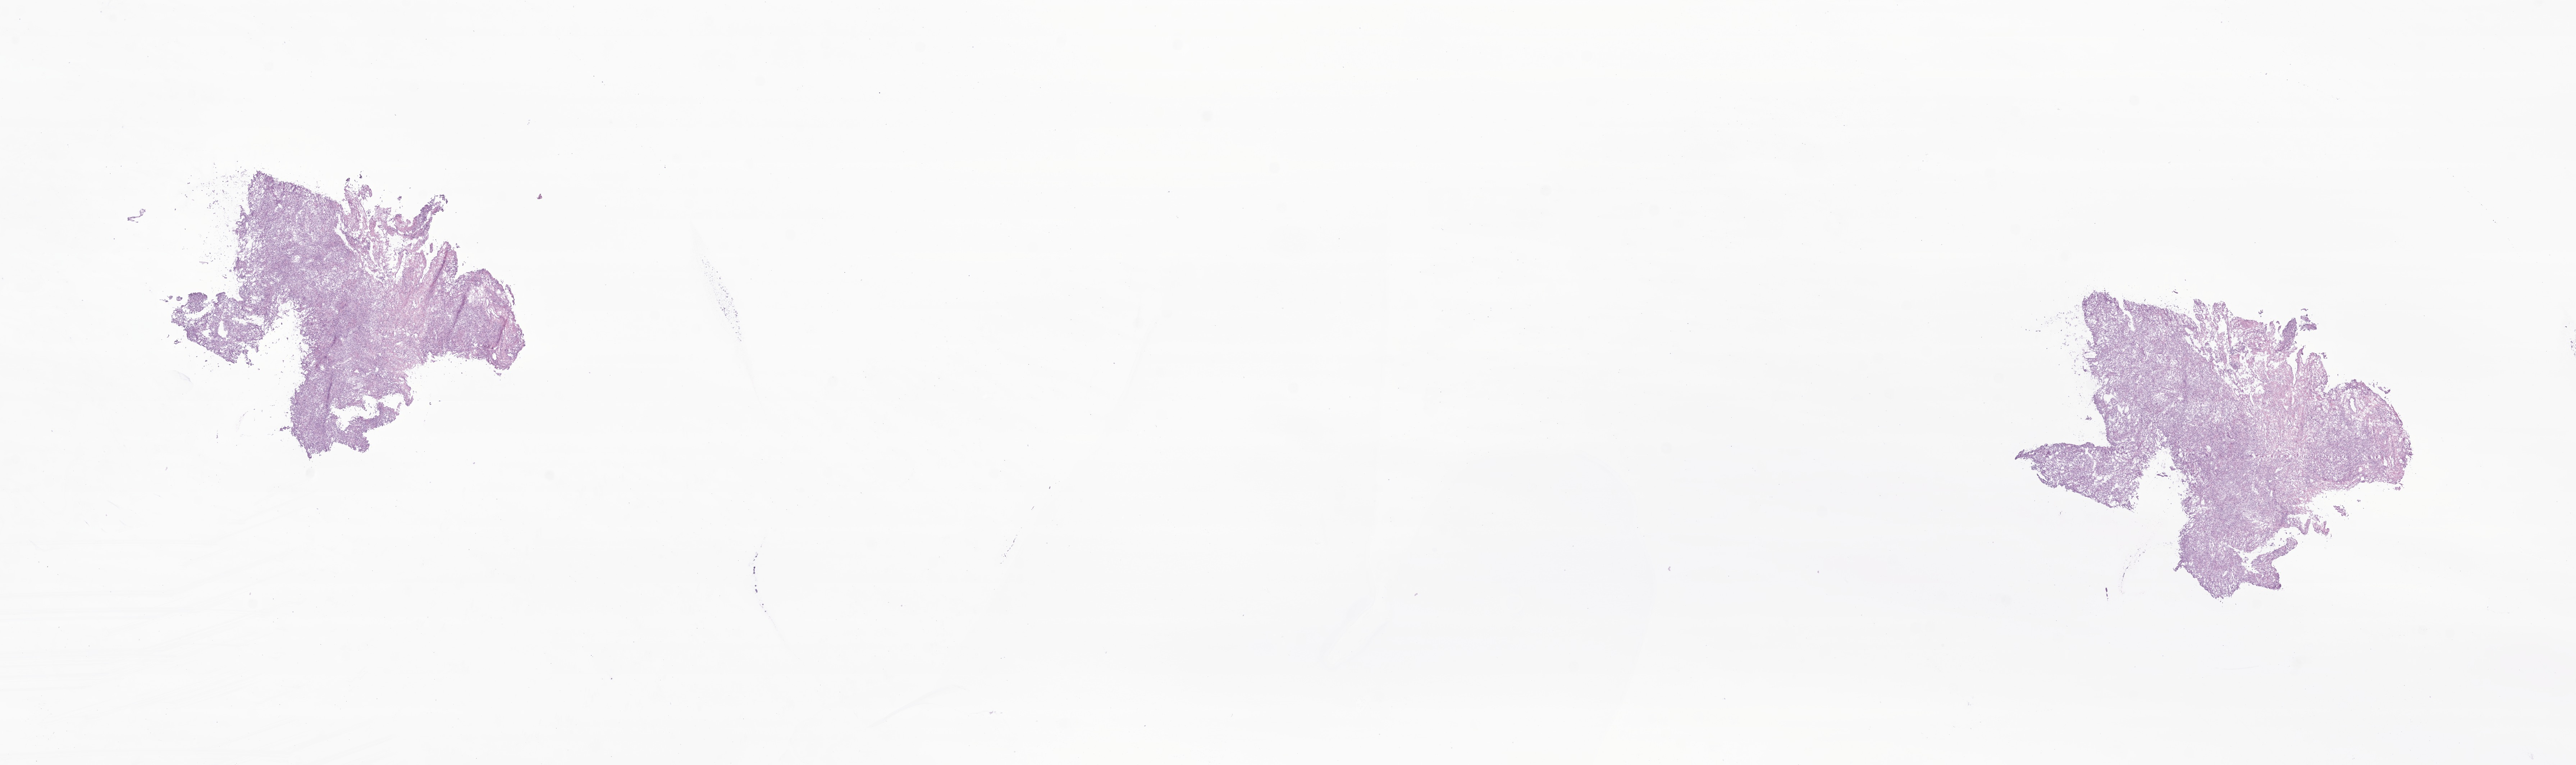
Whole-slide image, haematoxylin and eosin stain of tumor tissue from the ovary — whole scanned area (about 30.2 x 9.0 mm) shown as a low-resolution overview; frozen section. Patient female; age 187 months (15 years 7 months).
- recorded diagnosis: Sclerosing stromal tumor